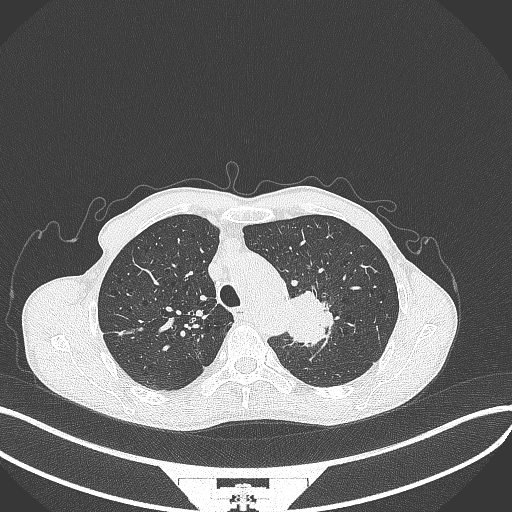
Chest CT, one axial slice; position 319 of 386 along the scan axis; reconstruction kernel B70f; 120 kVp; lung window (W 1500 / L -600 HU); 512 × 512 image matrix. Patient: male, 65 years. From the clinical record (not read from this slice): clinical TNM (as recorded): T2b N0 M0; histopathological grade: G2.
Structures marked on this image (rectangle marked by the reading radiologist):
- lung tumour (recorded histology: adenocarcinoma): bounding box [x1, y1, x2, y2] px = [287, 288, 335, 348]